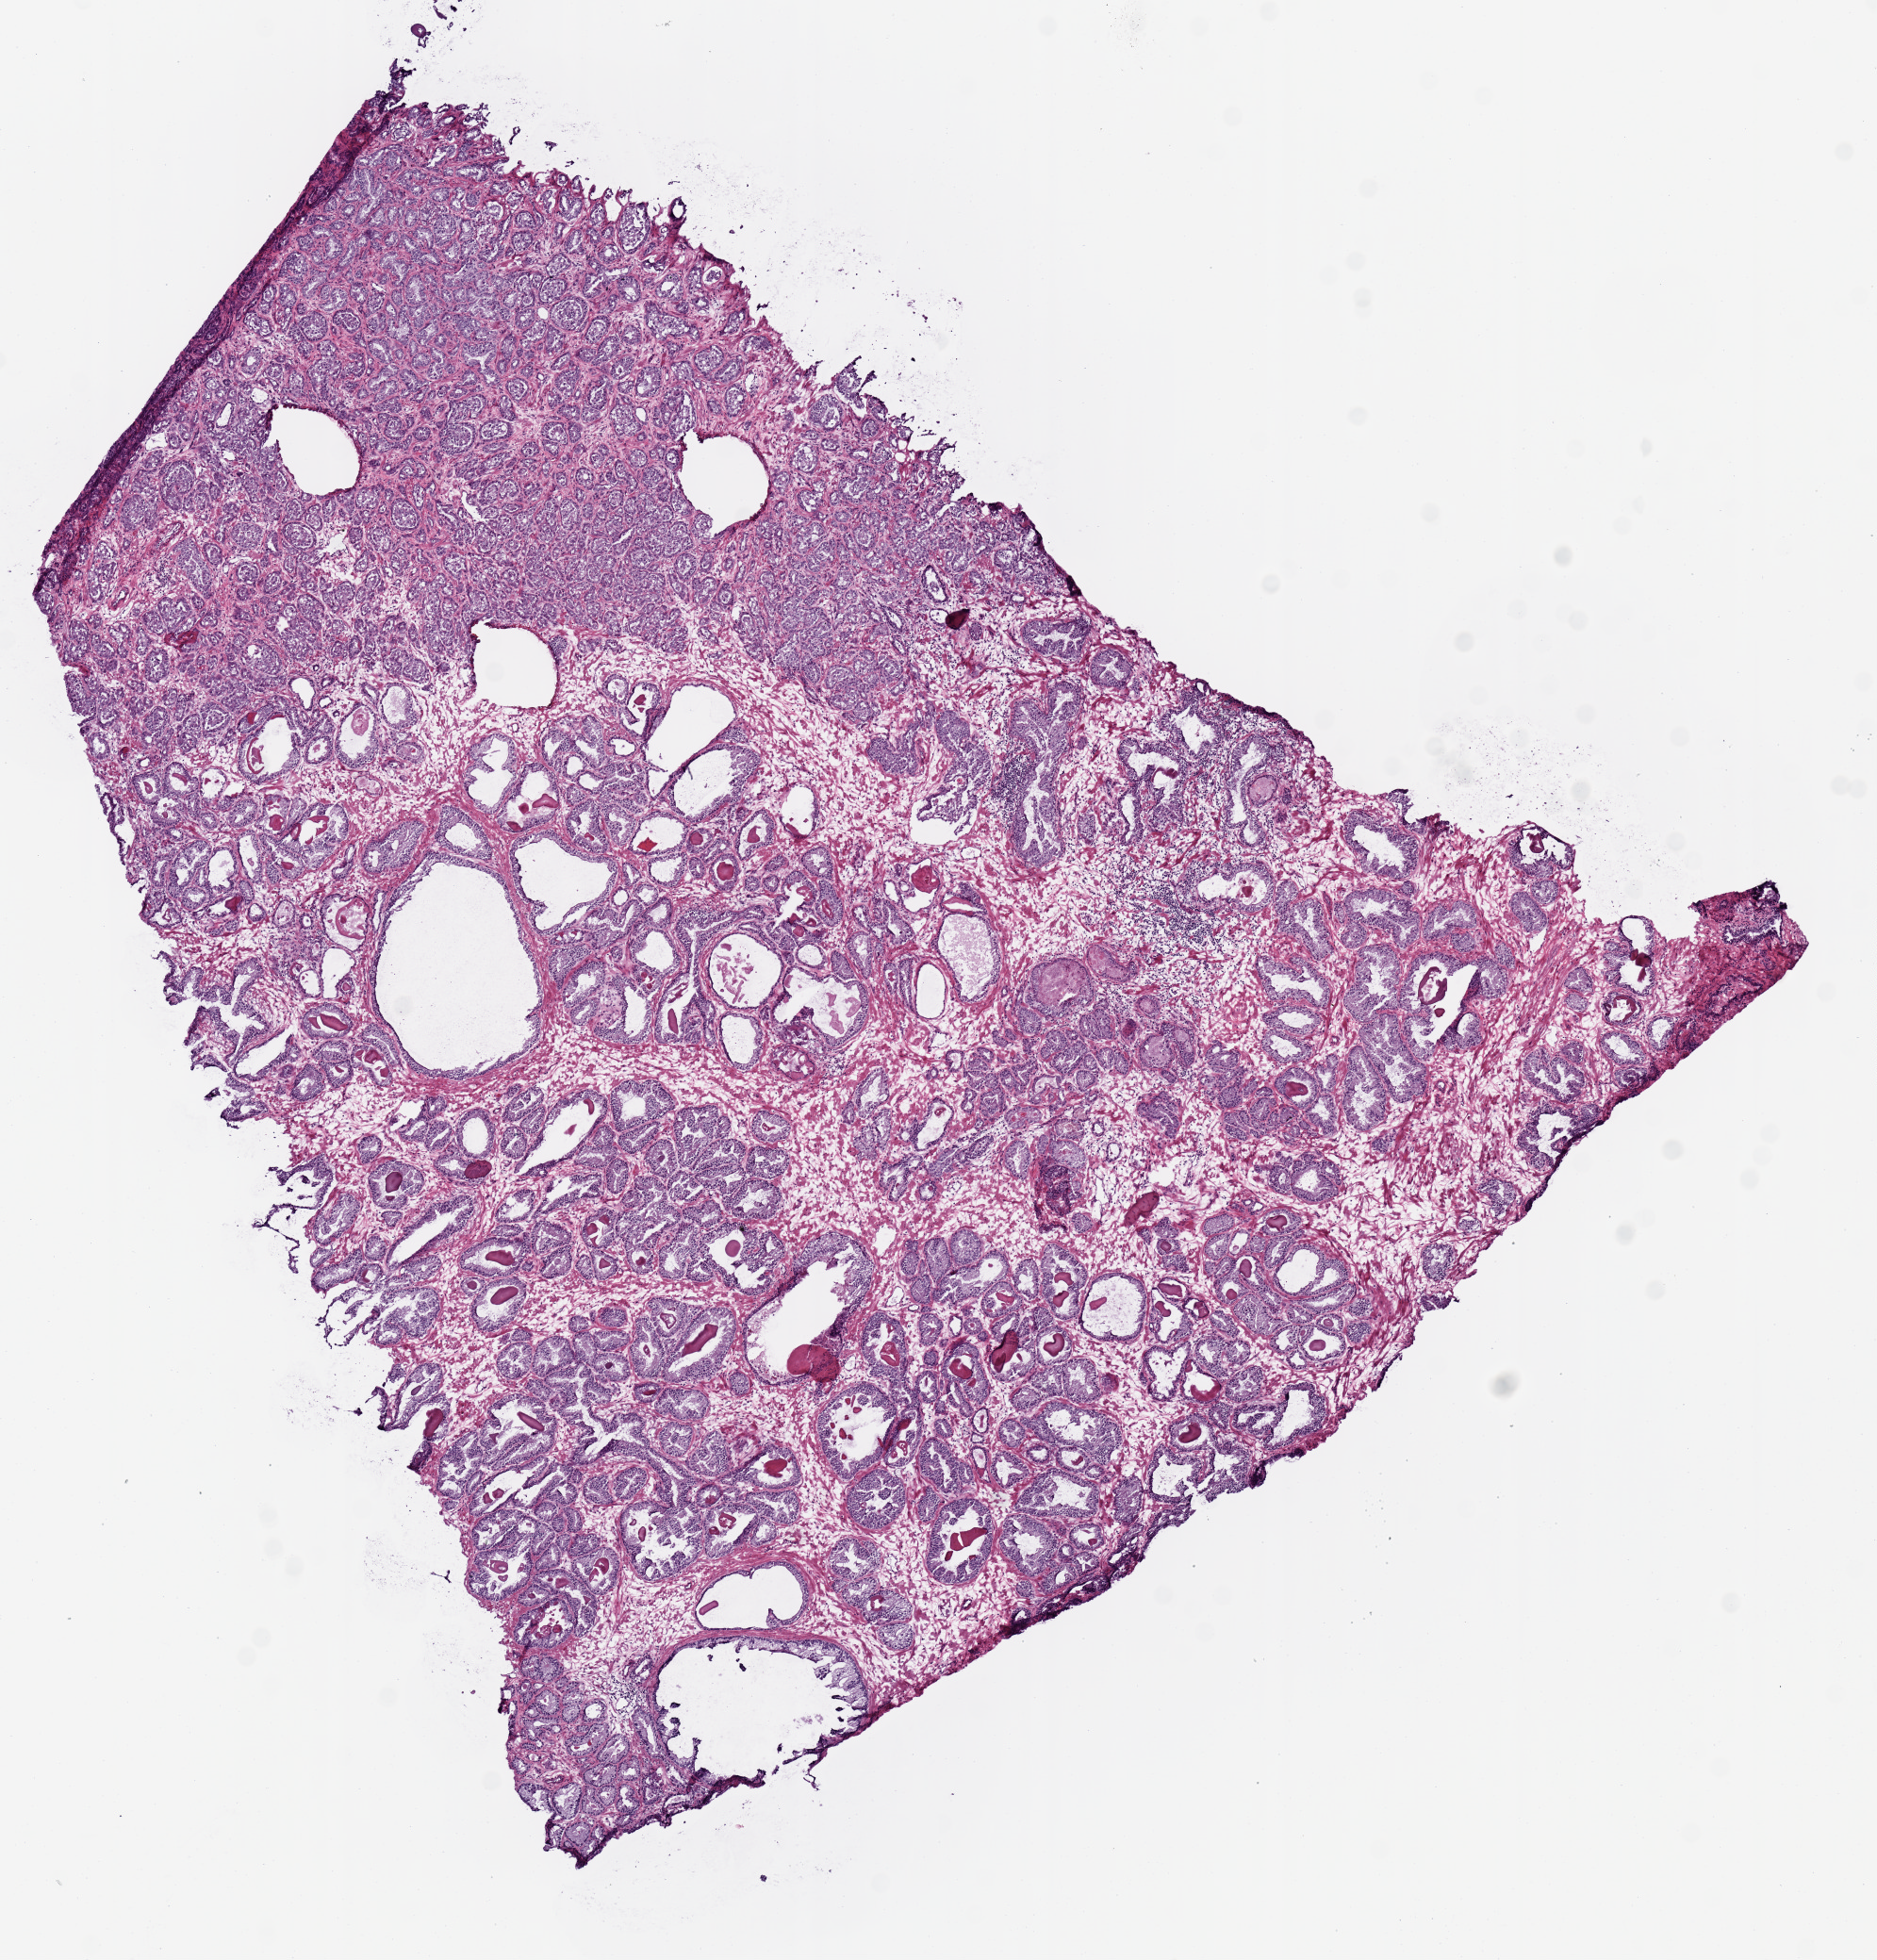
Digitized H&E tissue section (whole slide), a low-resolution overview of the entire scanned area, about 7.9 x 8.2 mm (slide scanned at 20x). Frozen section from the top of the tissue portion. Primary tumour sample from the prostate. Male patient; age at initial diagnosis 48 years.
Diagnosis: Acinar cell carcinoma.